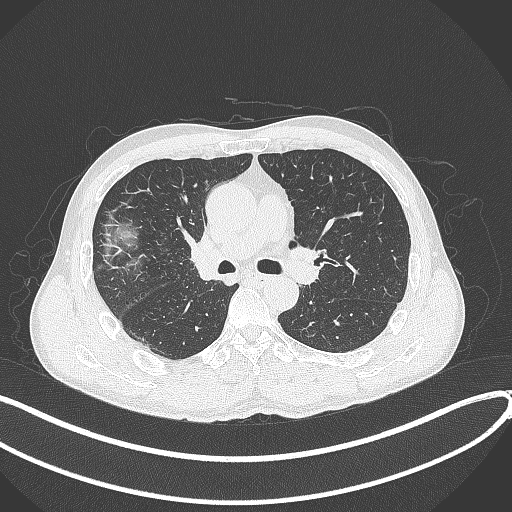
Chest CT, one axial slice. Position 233 of 409 along the scan axis. Reconstruction kernel B70f. Lung window (W 1500 / L -600 HU). 512 × 512 image matrix, field of view 400 × 400 mm. Patient: male, 53 years. From the clinical record (not read from this slice): clinical TNM (as recorded): T1b N0 M0.
Annotated regions visible in this slice (rectangle marked by the reading radiologist):
- lung tumour (recorded histology: squamous cell carcinoma): bounding box (x1, y1, x2, y2) in pixels: (182, 227, 222, 286)